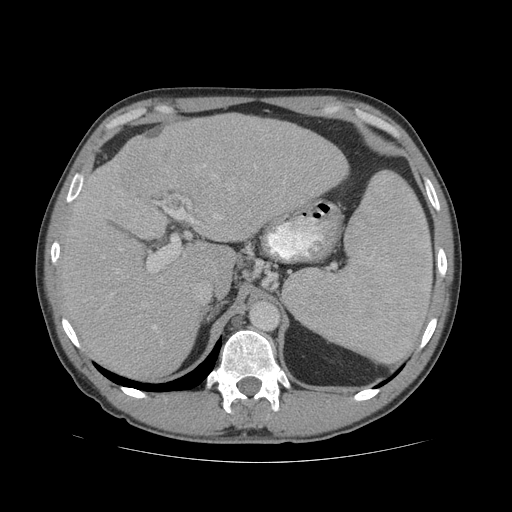
Contrast-enhanced abdominal CT (liver protocol), one axial slice. Position 45 of 81 along the scan axis. Reconstruction kernel STANDARD. 140 kVp. Soft-tissue window (W 400 / L 40 HU). 512 × 512 image matrix, field of view 400 × 400 mm. Case-level facts recorded for this patient, not image findings: diagnosis: hepatocellular carcinoma (patient treated with transarterial chemoembolisation; whether this scan precedes or follows treatment is not stated here); TNM stage (as recorded): Stage-IVB; Child-Pugh class: B.
Outlined on this slice (semi-automatically segmented with operator editing):
- liver parenchyma outside the tumour (the mass and vessels are separate outlines, so this box may not span the whole liver): bounding box [x1, y1, x2, y2] px = [58, 114, 348, 380]
- mass: [109, 136, 174, 203]
- liver vessels: [108, 165, 257, 330]